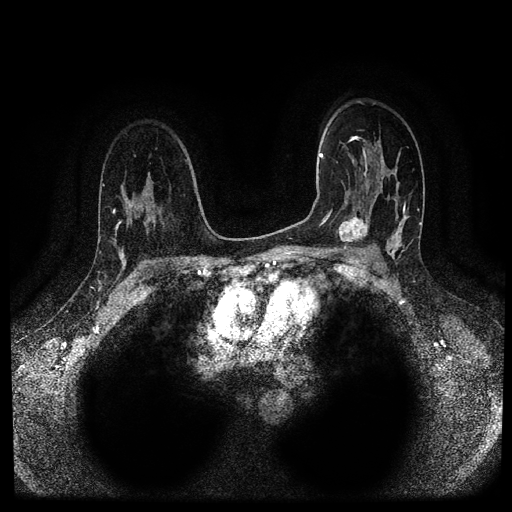
Breast MRI (dynamic contrast-enhanced, multi-phase), one axial slice. Slice 68 of 116 in the series (ordered by position). Dynamic contrast-enhanced series, time point 2 of 5 at this slice position (early post-contrast). 1.5 T. TE 2.6 ms, TR 5.3 ms. 2 mm slice thickness. 512 × 512 image matrix, field of view 350 × 350 mm. Female patient, age 44 years.
Outlined on this slice (semi-automatic segmentation, software-assisted and operator-edited):
- breast lesion (labelled 'tumour' in the annotation; benign lesions carry a separate 'benign' label): box from (x=335, y=212) to (x=370, y=247) px